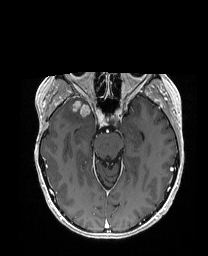
Brain MRI from a brain-tumour surgery series, one axial slice. Slice 113 of 192 in the series (ordered by position). T1-weighted post-contrast. 1 mm slice thickness. 208 × 256 image matrix, field of view 203 × 250 mm. Case-level facts recorded for this patient, not image findings: histopathology: Metastatic Carcinoma from Breast primary; tumour location: Right Frontal.
Outlined on this slice (manually delineated by an expert):
- tumour: box from (x=77, y=99) to (x=96, y=114) px